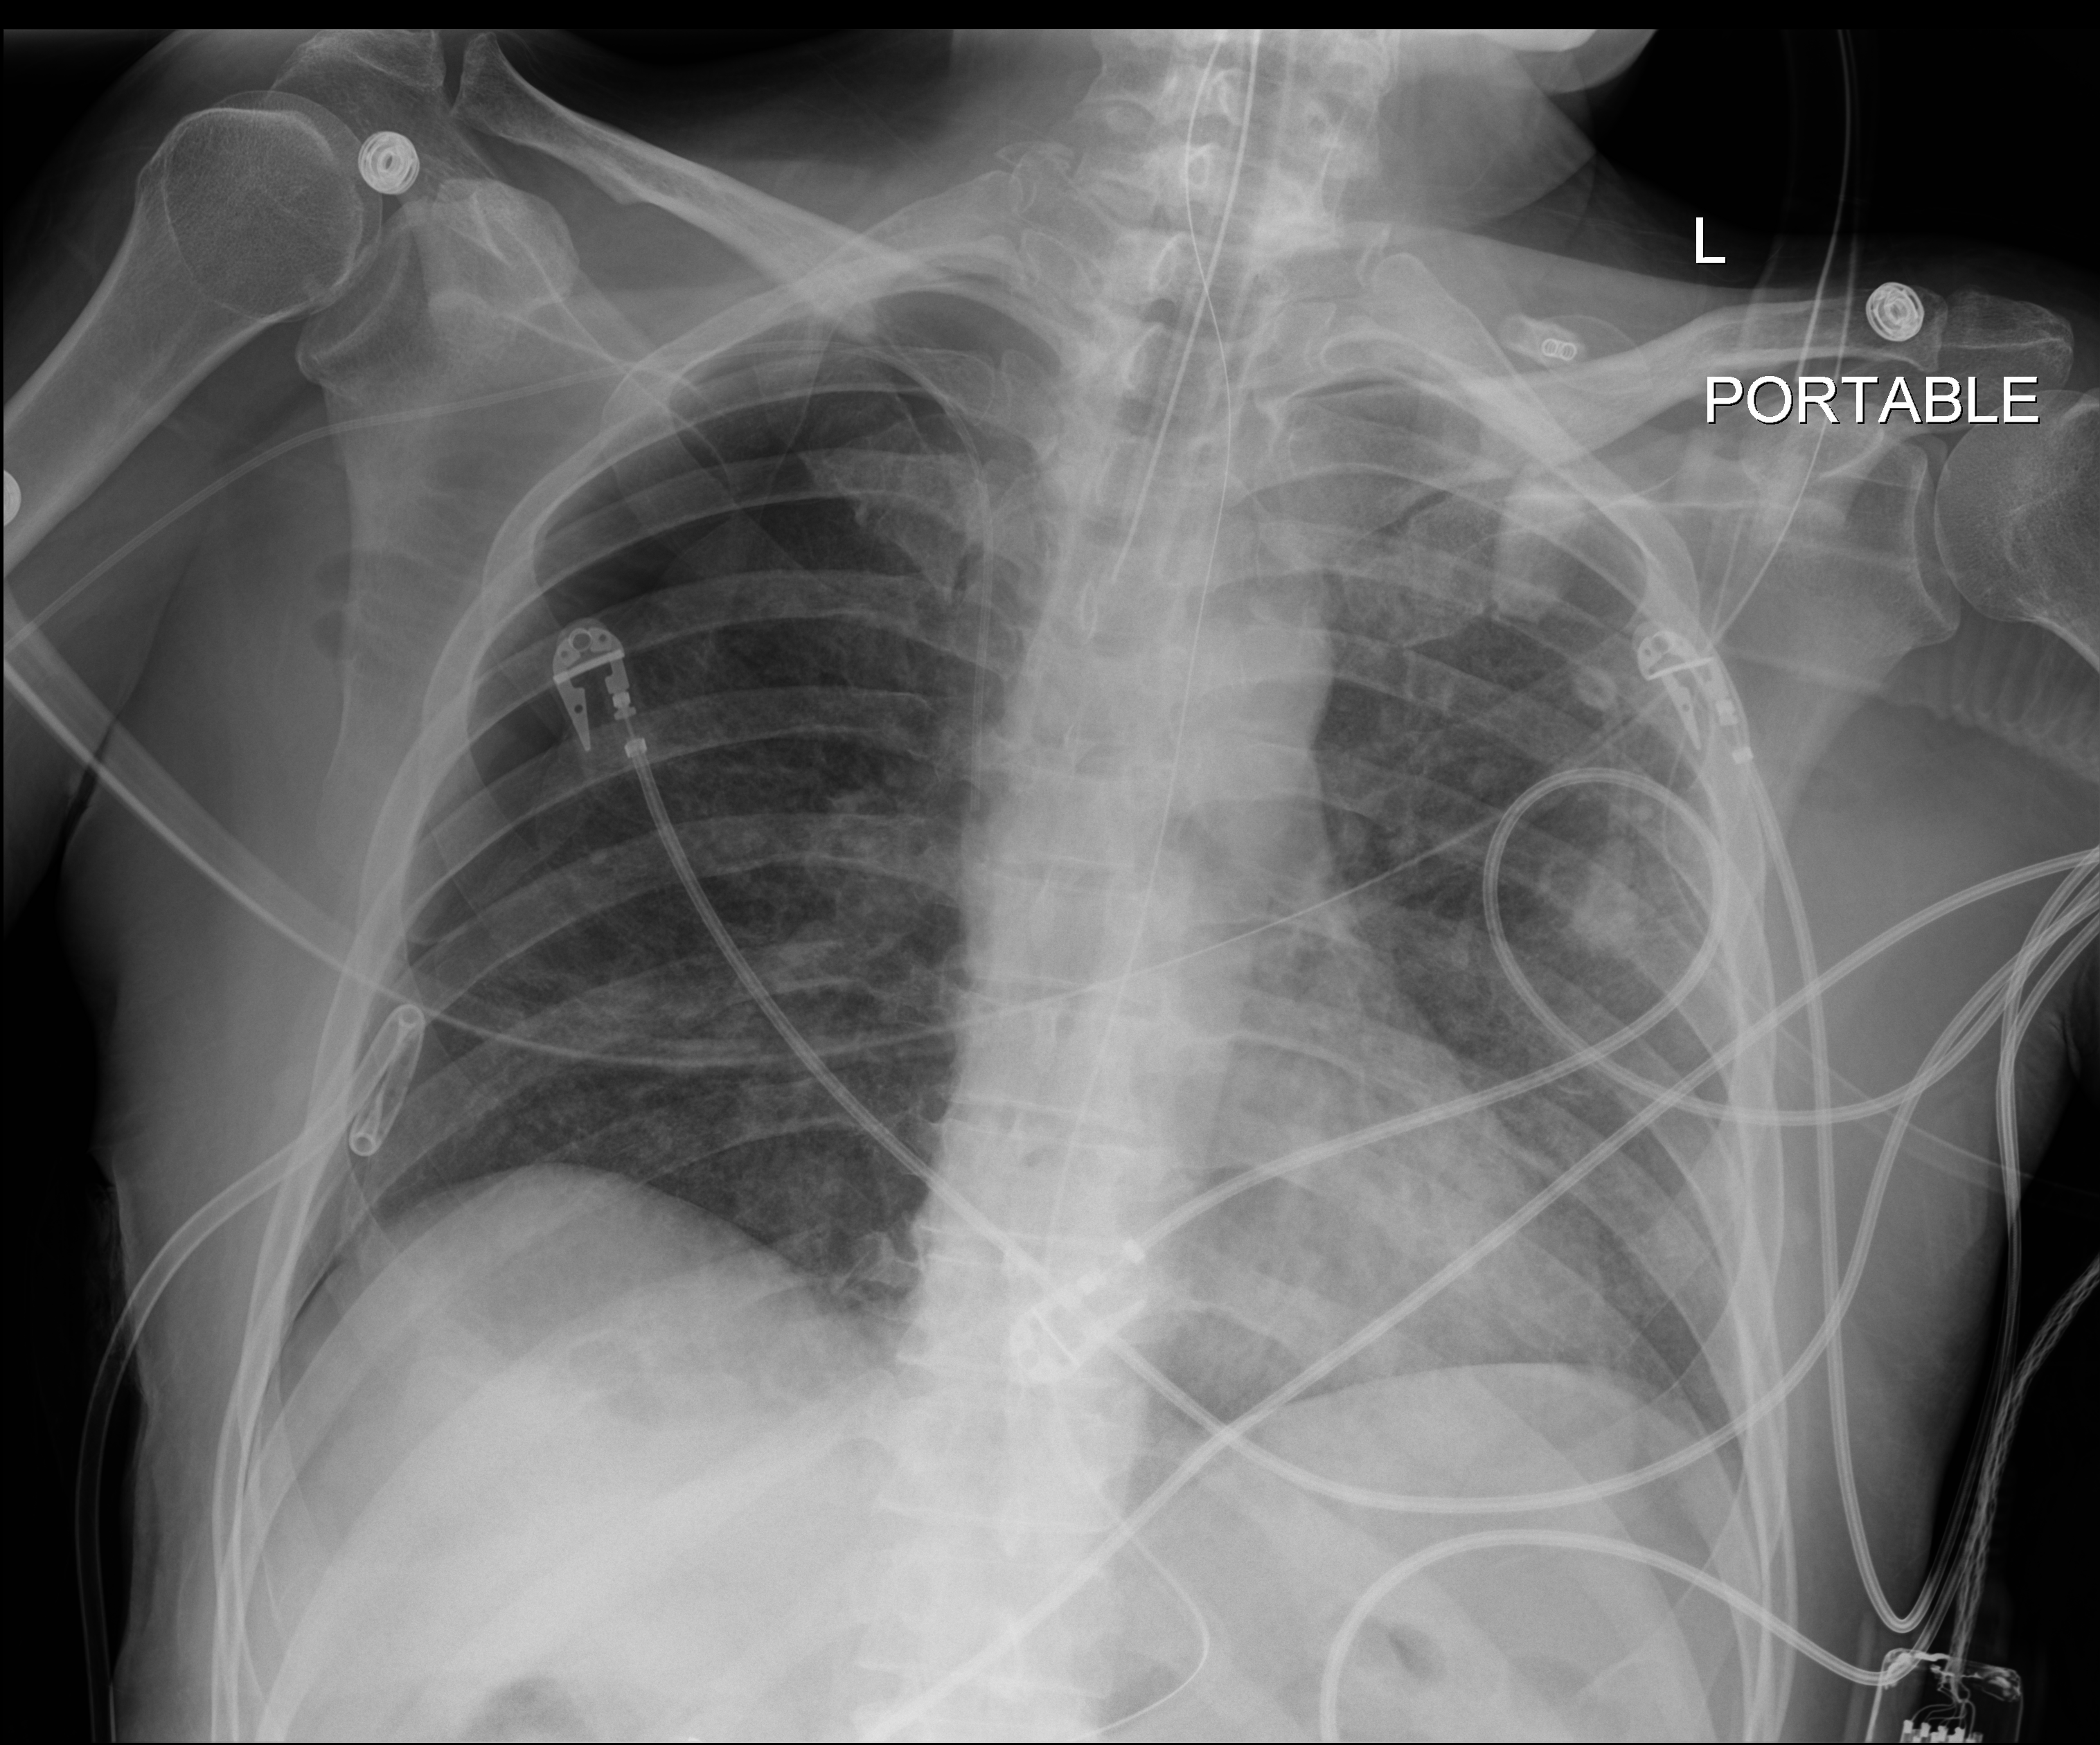
Bedside chest radiograph (digital radiography). Male patient hospitalised with COVID-19, age 18–59 years.
Admission-level facts for this patient (not findings on this image; timing relative to this image not recorded):
- hypertension (admission record): no
- length of hospital stay: 77 days